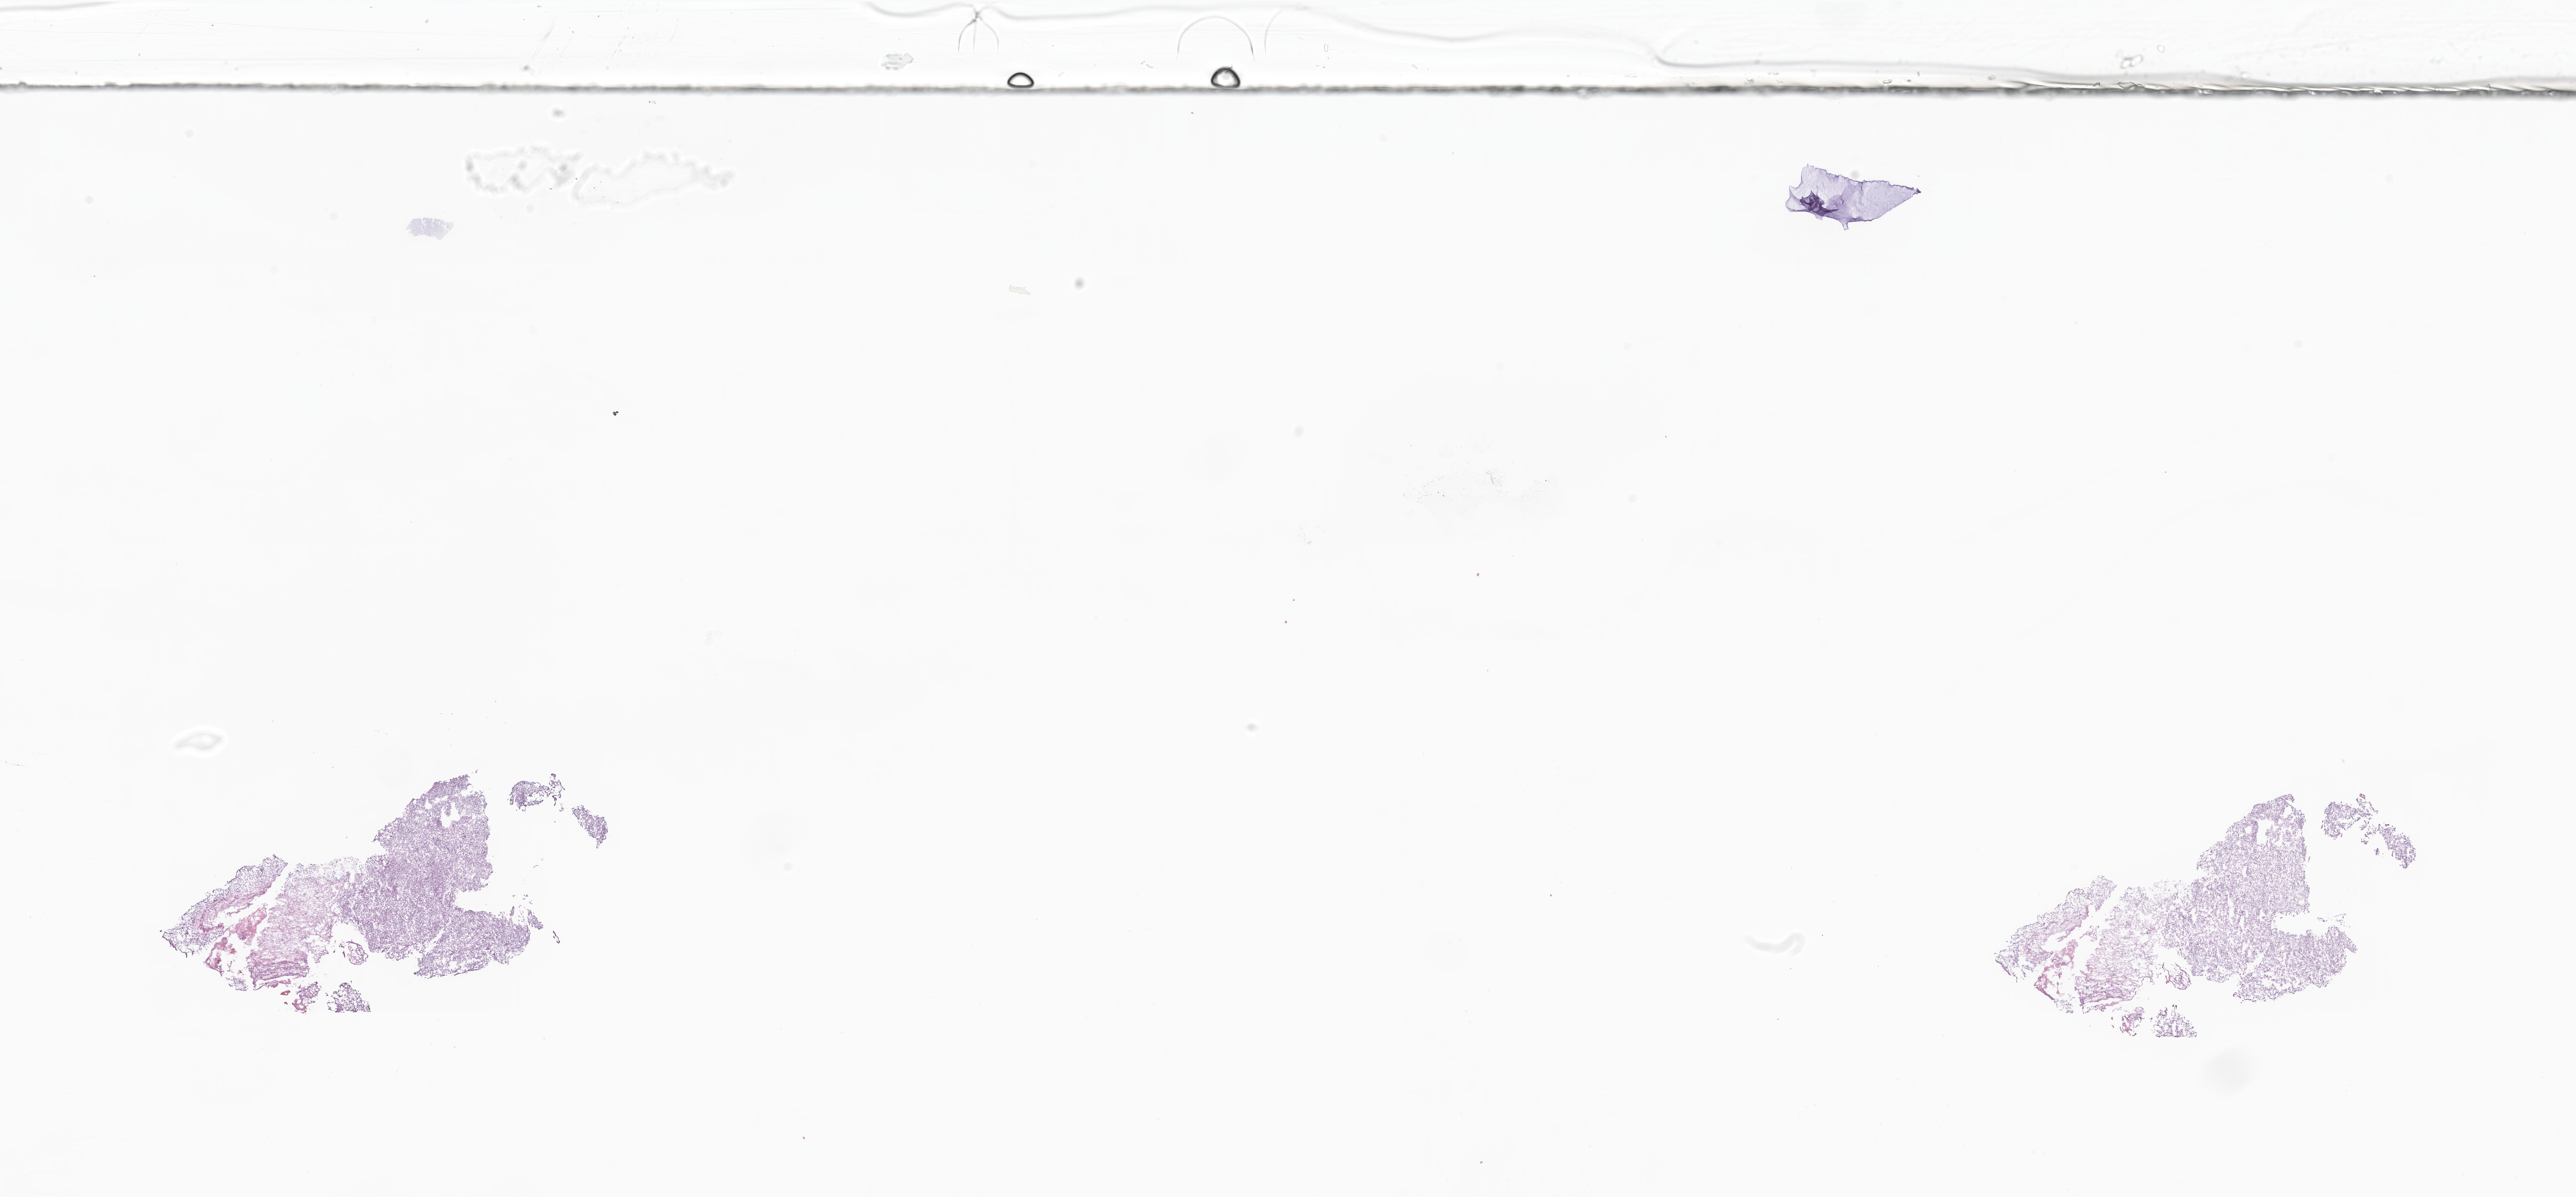
Whole-slide image, haematoxylin and eosin stain of tumor tissue — low-resolution overview of the scanned area, about 29.4 x 13.7 mm. Frozen section (OCT-embedded). Male patient, age 212 months (17 years 8 months).
Diagnosis: Sarcoma, NOS.